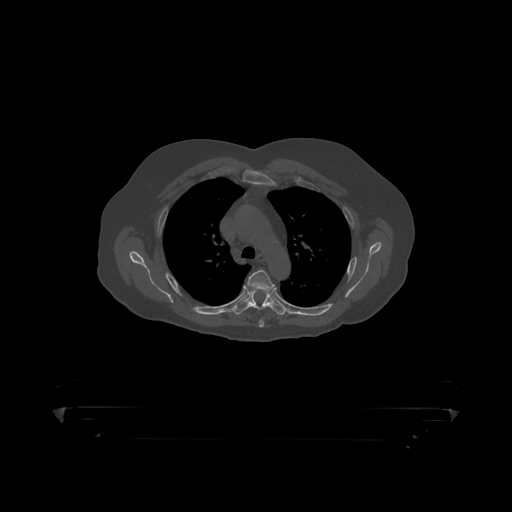
CT including the spine, one axial slice. Slice 329 of 390 in the series (ordered by position). Bone window (W 1800 / L 400 HU). 1.25 mm slice thickness. 512 × 512 image matrix, field of view 650 × 650 mm. Patient: male, 60 years. Case-level facts recorded for this patient, not image findings: primary cancer: prostate.
Annotated regions visible in this slice (semi-automatically segmented with operator editing):
- T4 vertebra: box from (x=247, y=270) to (x=276, y=293) px
- T5 vertebra: (x=233, y=291)–(x=287, y=316)